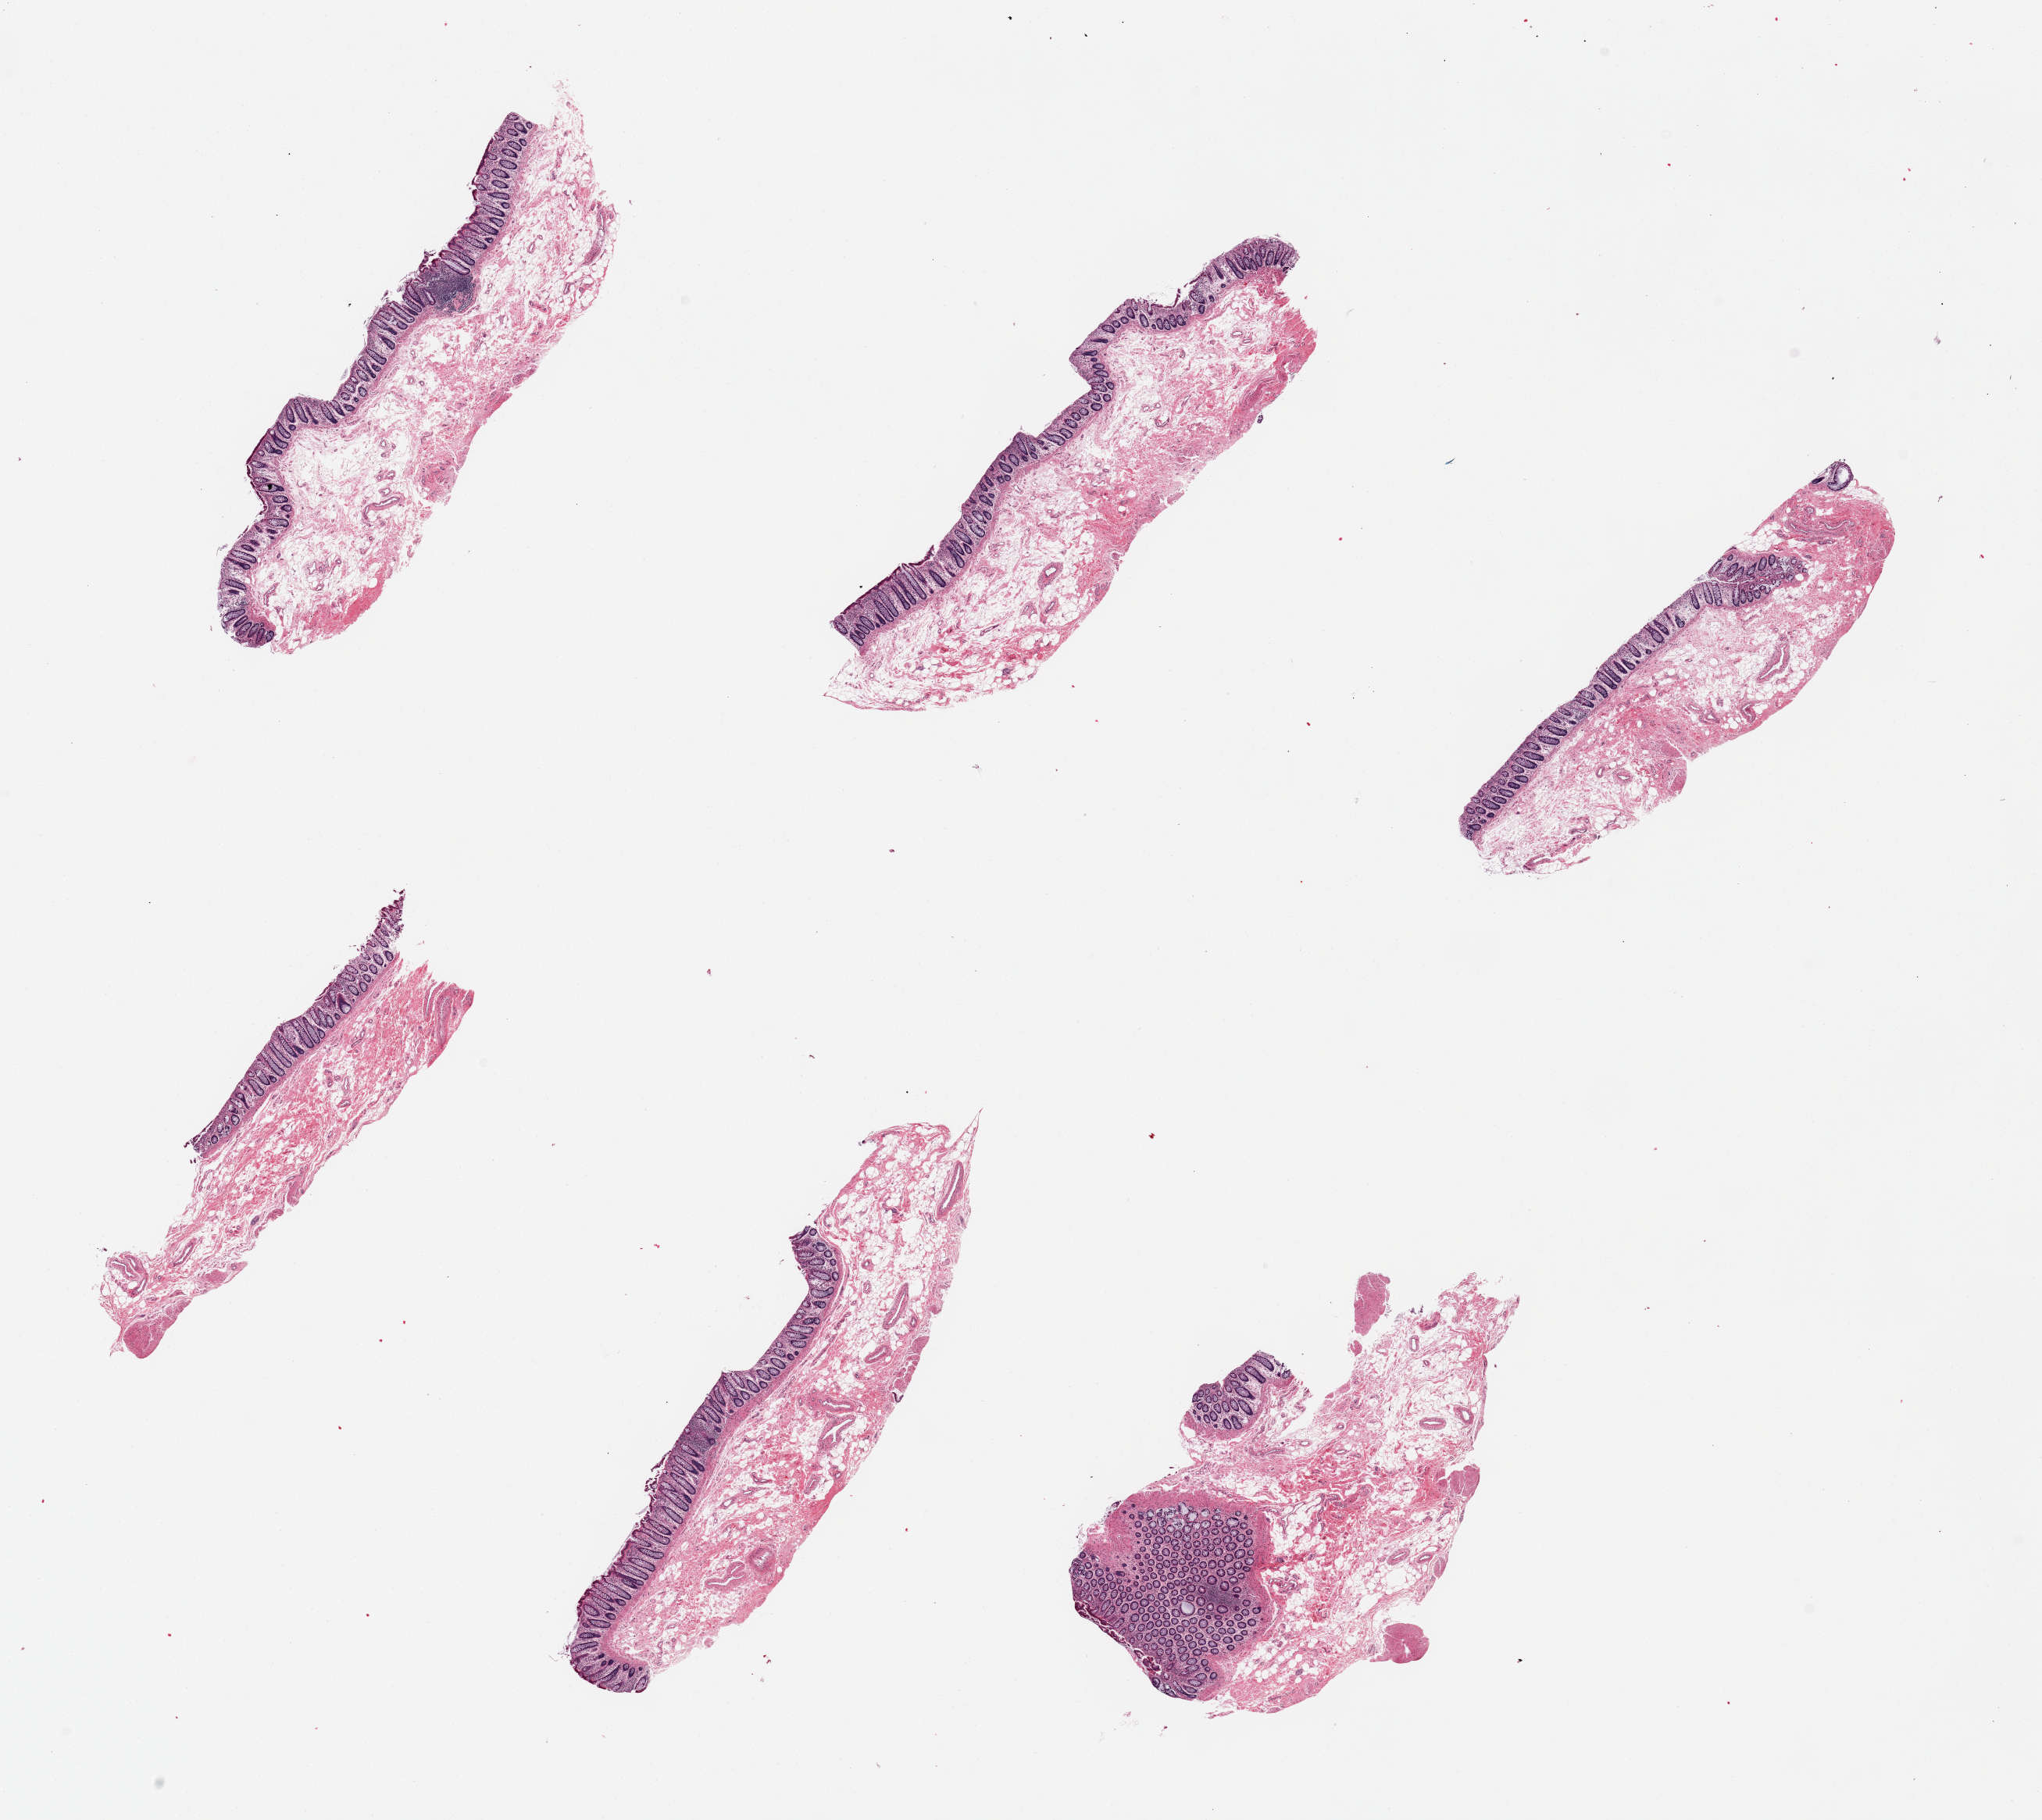
Whole-slide image, hematoxylin and eosin (H&E) stain — a low-resolution overview of the entire scanned area, about 20.7 x 18.4 mm (slide scanned at 20x), PAXgene-fixed, paraffin-embedded tissue, sampled site (target tissue): sigmoid colon, tissue donor sample. Male donor.
Review note (as recorded): 6 pieces, mucosa and submucosa (not target) with only scant muscularis (target).